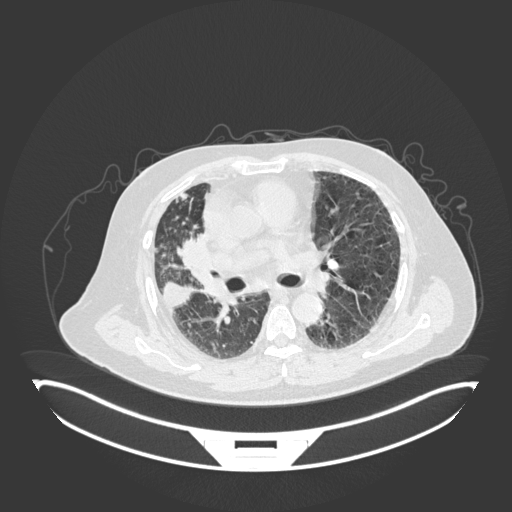
Chest CT, one axial slice; slice 89 of 201 in the series (ordered by position); 120 kVp; lung window (W 1500 / L -600 HU); 1 mm slice thickness; 512 × 512 image matrix, field of view 500 × 500 mm. Male patient, age 69 years. Case-level facts recorded for this patient, not image findings: clinical TNM (as recorded): T4 N3 M1.
Structures marked on this image (bounding box drawn by a radiologist):
- lung tumour (recorded histology: adenocarcinoma): box from (x=178, y=231) to (x=214, y=278) px